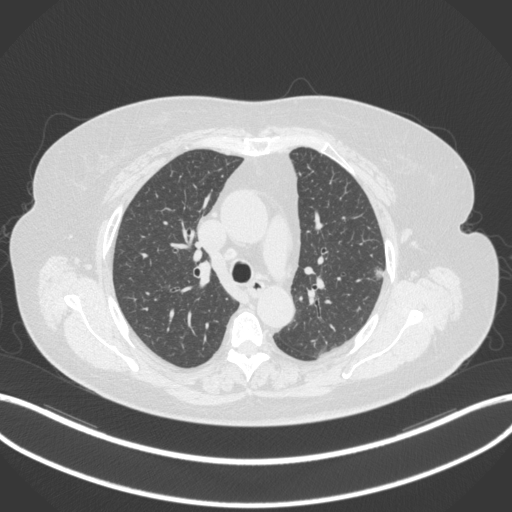
Chest CT, one axial slice; position 220 of 310 along the scan axis; reconstruction kernel B31f; 120 kVp; lung window (W 1500 / L -600 HU); 1 mm slice thickness; 512 × 512 image matrix, field of view 400 × 400 mm. Patient: female, 70 years. Case-level facts recorded for this patient, not image findings: clinical TNM (as recorded): T1c N0 M0.
Outlined on this slice (bounding box drawn by a radiologist):
- lung tumour (recorded histology: adenocarcinoma): bounding box <369,264,387,285> (left, top, right, bottom; pixels)